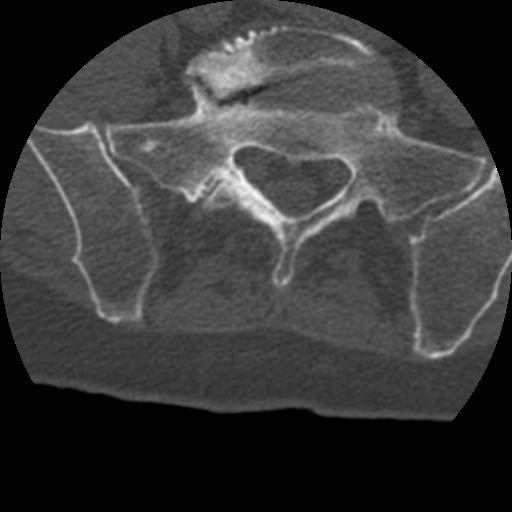
CT including the spine, one axial slice. Slice 29 of 399 in the series (ordered by position). Bone window (W 1800 / L 400 HU). 512 × 512 image matrix, field of view 160 × 160 mm. Patient age 69 years. Case-level facts recorded for this patient, not image findings: primary cancer: prostate.
Structures marked on this image (semi-automatically segmented with operator editing):
- L5 vertebra: bounding box (x1, y1, x2, y2) in pixels: (189, 26, 378, 210)